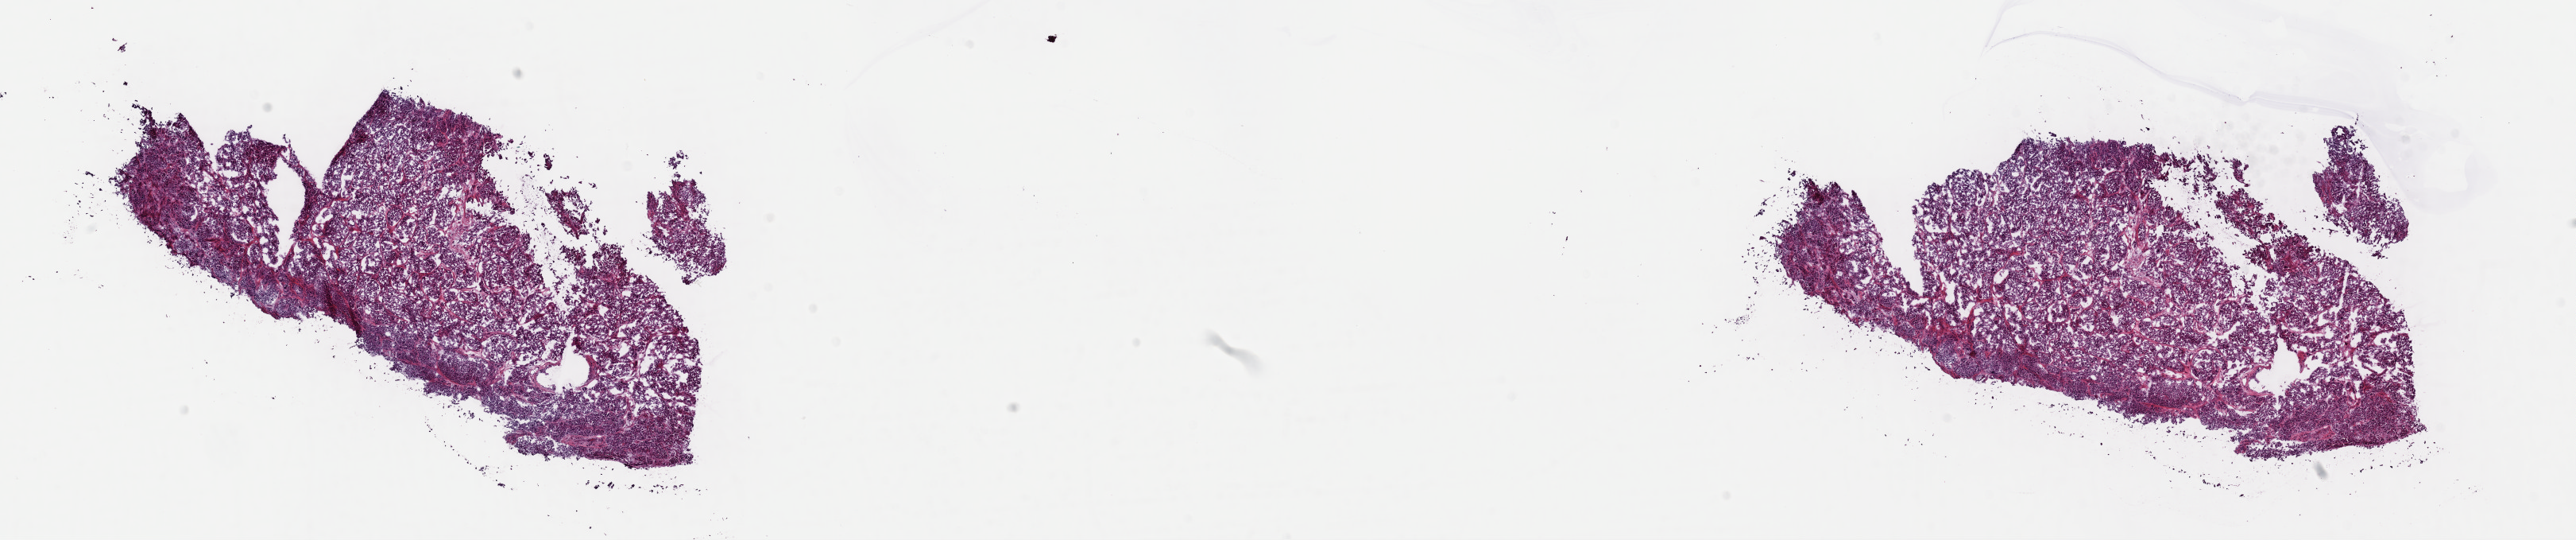
H&E whole-slide image, shown as a low-resolution overview of the whole scanned area (about 25.6 x 5.4 mm), frozen section, bladder, primary tumour sample. Patient: male, age at initial diagnosis 76 years. Histologic grade: high grade. Pathologist review of this section (percent, as recorded): tumour cells 90%, tumour nuclei 90%, normal cells 0%, stromal cells 9%, necrosis 1%. Infiltration values recorded for this section: lymphocyte infiltration 1%, monocyte infiltration 1%, neutrophil infiltration 1%.
AJCC pathologic stage: IV (7th edition). Histologic diagnosis: Transitional cell carcinoma. TNM: T3b N2 MX. Lymph nodes positive (case pathology): 8 of 17 examined.